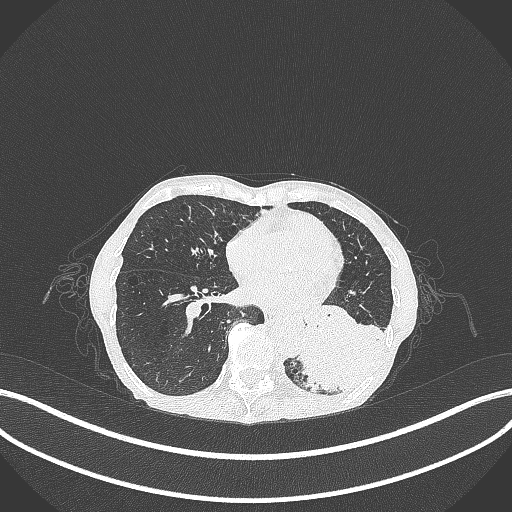
Chest CT, one axial slice; slice 100 of 347 in the series (ordered by position); 120 kVp; lung window (W 1500 / L -600 HU); 1 mm slice thickness; 512 × 512 image matrix, field of view 400 × 400 mm. Female patient, age 70 years. Case-level facts recorded for this patient, not image findings: clinical TNM (as recorded): T3 N0 M0.
Annotated regions visible in this slice (bounding box drawn by a radiologist):
- lung tumour (recorded histology: small cell carcinoma): bounding box <301,321,399,398> (left, top, right, bottom; pixels)